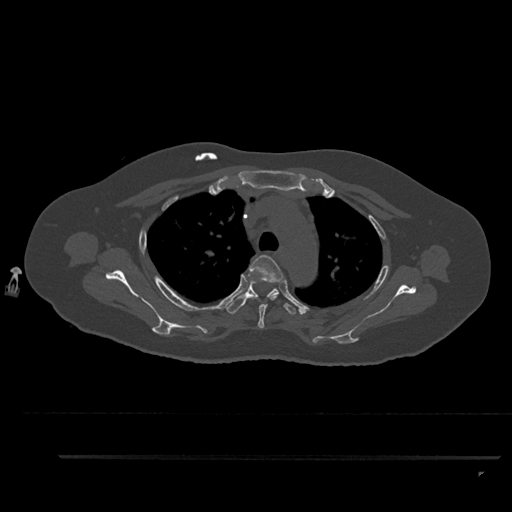
CT including the spine, one axial slice. Bone window (W 1800 / L 400 HU). 512 × 512 image matrix, field of view 408 × 408 mm. Patient: female, 44 years. From the clinical record (not read from this slice): primary cancer: renal; vertebrae with lytic lesions (as recorded): L1.
Structures marked on this image (semi-automatic segmentation, software-assisted and operator-edited):
- T3 vertebra: bounding box <248,255,283,328> (left, top, right, bottom; pixels)
- T4 vertebra: <226,280,300,315>